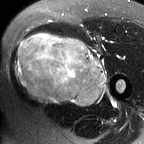
MRI of an extremity soft-tissue mass, one axial slice; slice 33 of 60 in the series (ordered by position); T2-weighted fat-saturated; MR volume resampled by the dataset authors to the PET/CT grid (not the native acquisition matrix); 3.27 mm slice thickness; 144 × 144 image matrix, field of view 141 × 141 mm. Female patient. Case-level facts recorded for this patient, not image findings: histological type: pleiomorphic leiomyosarcoma; grade: intermediate; site of the primary tumour: left thigh.
Annotated regions visible in this slice (expert contour drawn on MRI and transferred to this co-registered scan by the dataset authors):
- gross tumour volume including surrounding oedema: box from (x=15, y=33) to (x=105, y=107) px
- gross tumour volume (mass): (x=15, y=35)–(x=105, y=105)